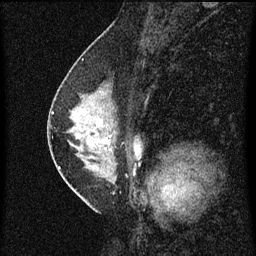
Breast MRI (dynamic contrast-enhanced), one sagittal slice; position 32 of 60 along the scan axis; dynamic contrast-enhanced series, image 2 of 3 at this slice position (ordered by acquisition); 1.5 T; TE 4.2 ms, TR 8 ms; 2 mm slice thickness; 256 × 256 image matrix, field of view 180 × 180 mm. Female patient, age 47 years.
Annotated regions visible in this slice (semi-automatically segmented with operator editing):
- analysis volume of interest (the breast-tissue region the enhancement analysis was run in; not a lesion): bounding box <54,80,139,187> (left, top, right, bottom; pixels)
- tumour enhancement mask (voxels above the 70 % enhancement threshold inside the analysis volume of interest): <59,146,138,169>